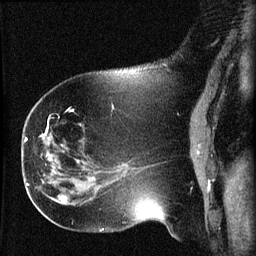
Breast MRI (dynamic contrast-enhanced), one sagittal slice; slice 22 of 60 in the series (ordered by position); dynamic contrast-enhanced series, image 2 of 3 at this slice position (ordered by acquisition); 1.5 T; TE 4.2 ms, TR 8.2 ms; 2 mm slice thickness; 256 × 256 image matrix. Patient: female, 63 years.
Annotated regions visible in this slice (semi-automatically segmented with operator editing):
- analysis volume of interest (the breast-tissue region the enhancement analysis was run in; not a lesion): bounding box <22,156,64,202> (left, top, right, bottom; pixels)
- tumour enhancement mask (voxels above the 70 % enhancement threshold inside the analysis volume of interest): <59,197,64,200>